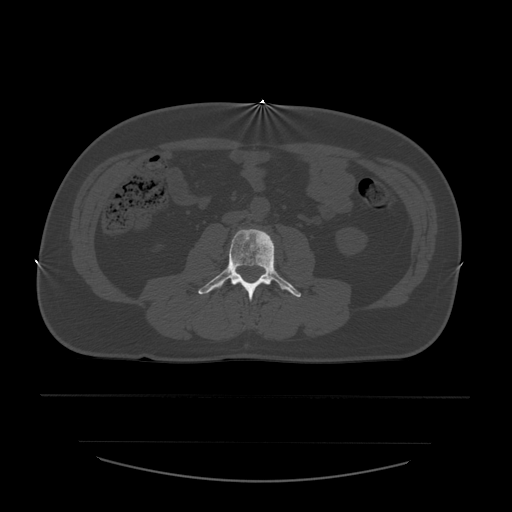
CT including the spine, one axial slice. Position 175 of 532 along the scan axis. Reconstruction kernel STANDARD. 120 kVp. Bone window (W 1800 / L 400 HU). 512 × 512 image matrix, field of view 441 × 441 mm. Patient age 44 years. From the clinical record (not read from this slice): primary cancer: soft tissue sarcoma.
Structures marked on this image (semi-automatic segmentation, software-assisted and operator-edited):
- L3 vertebra: bounding box [x1, y1, x2, y2] px = [198, 229, 302, 300]